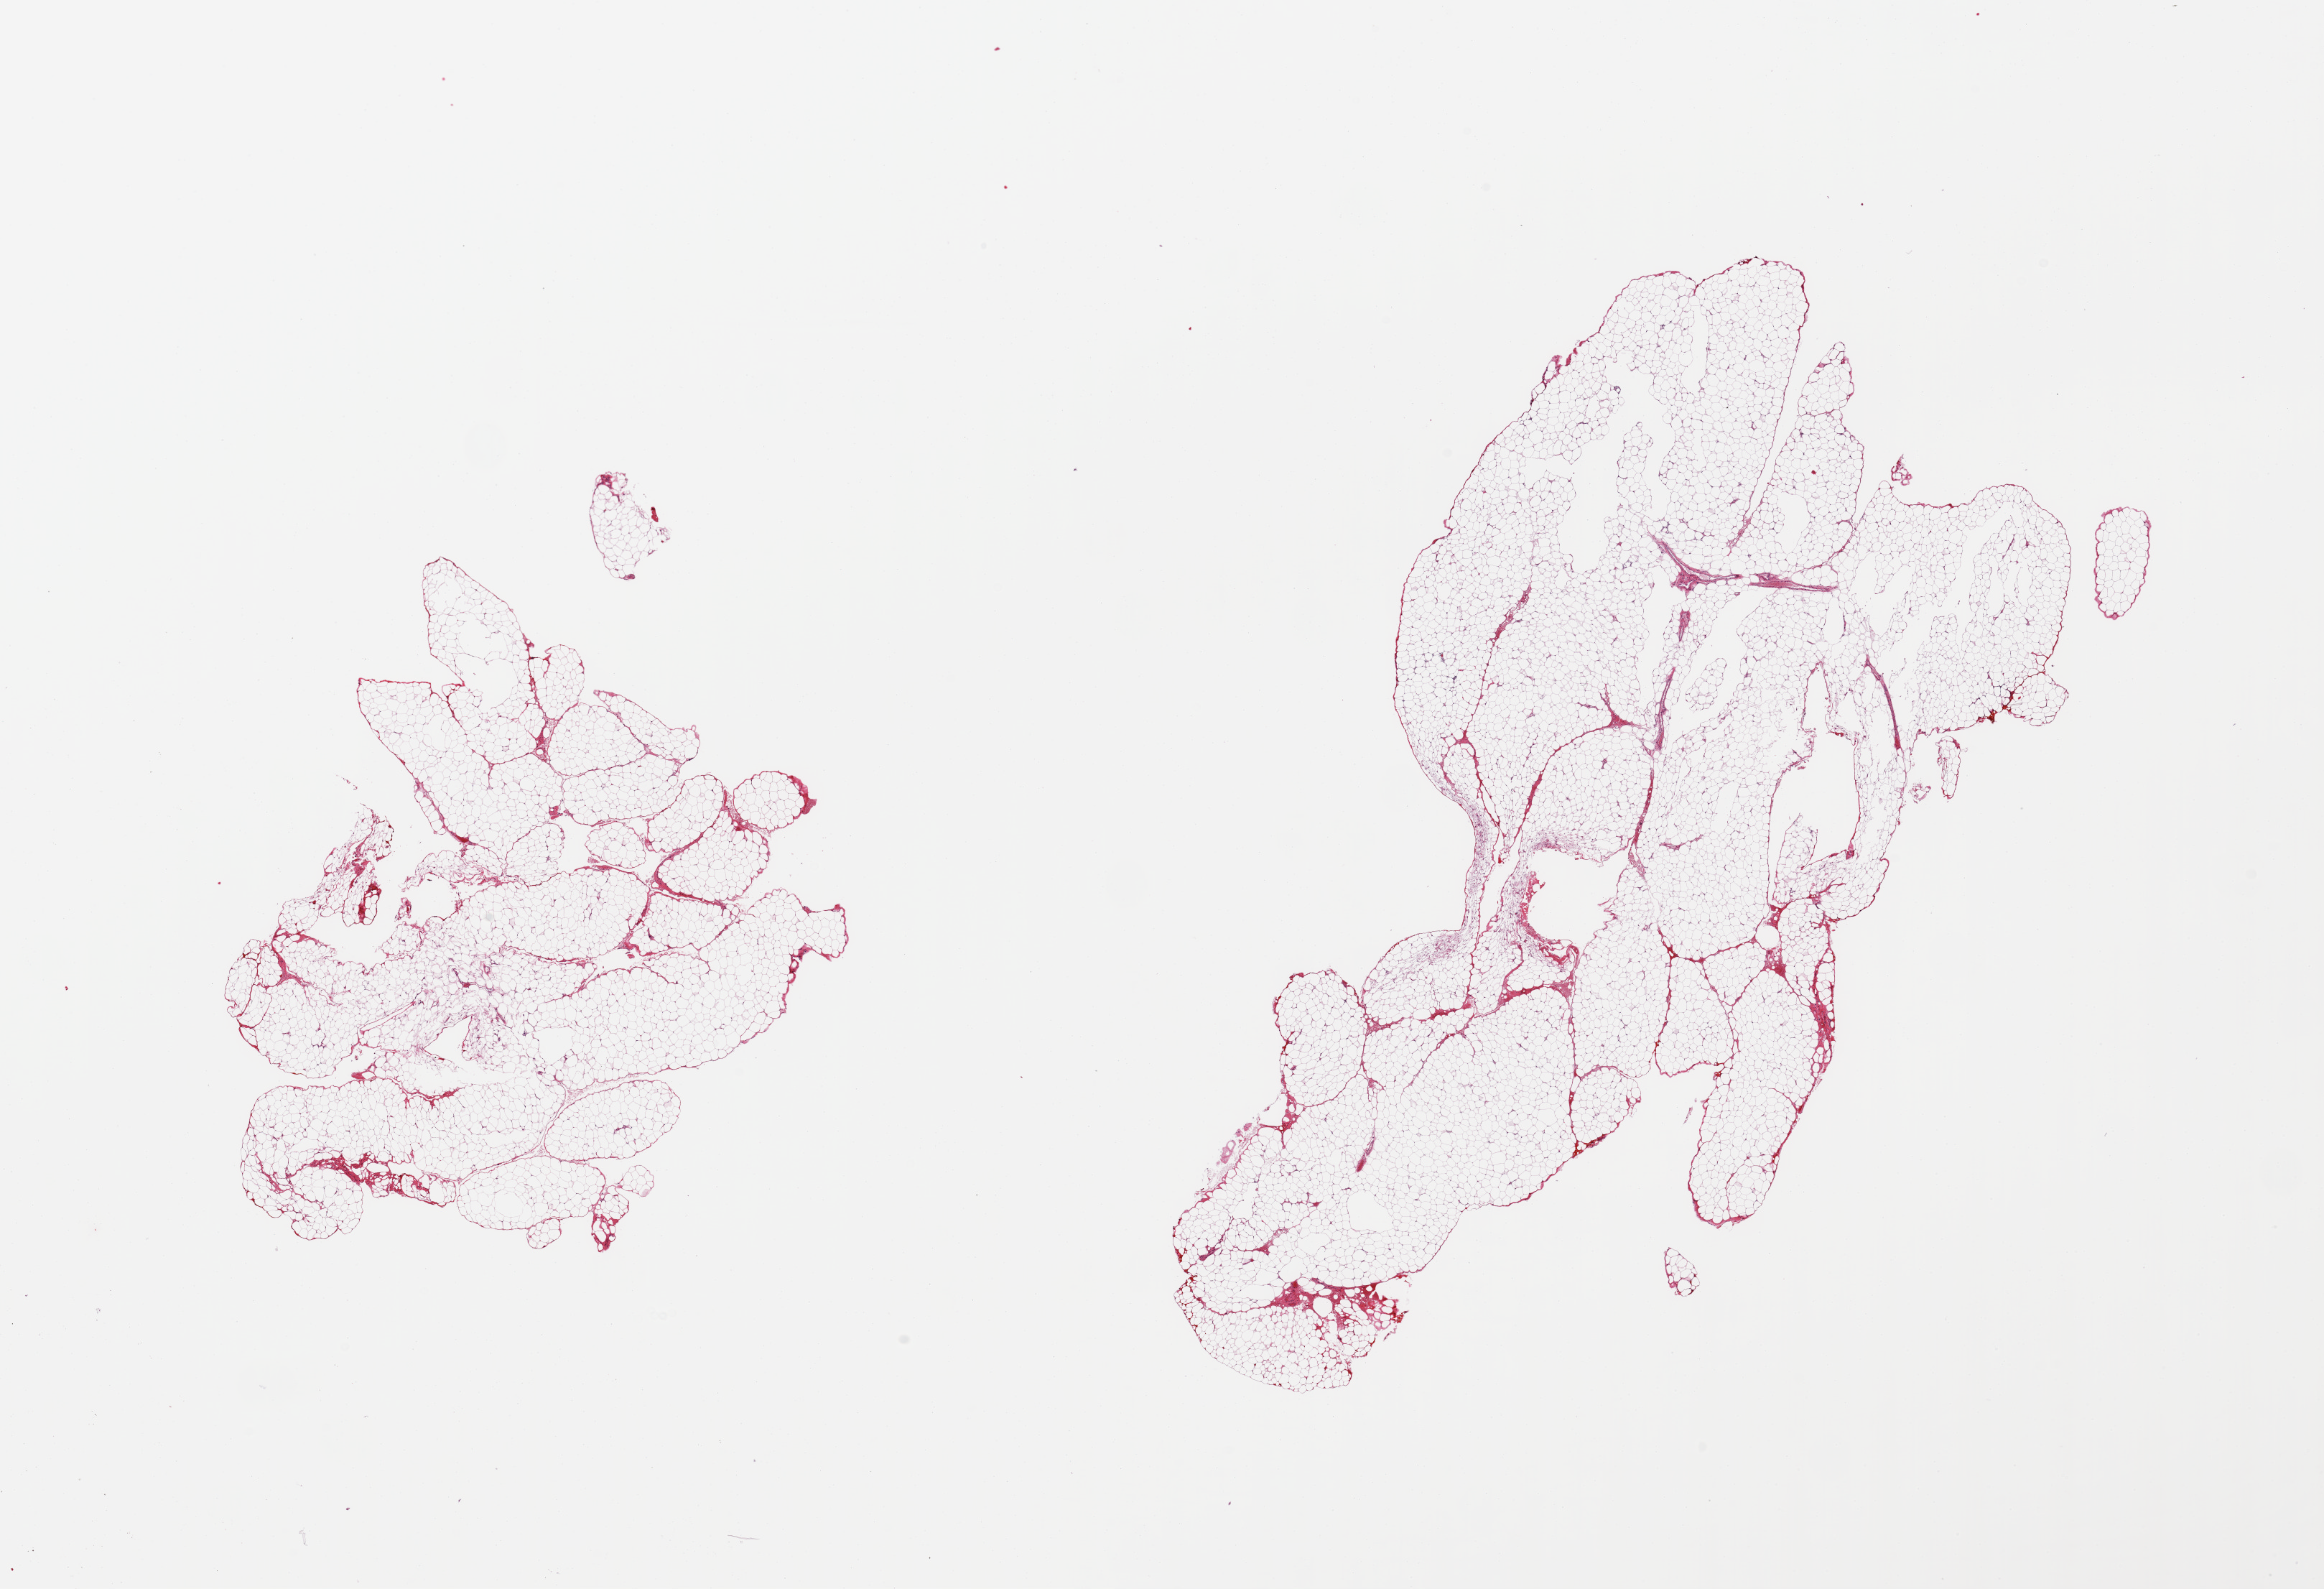
H&E whole-slide image, low-resolution overview of the scanned area, about 25.6 x 17.5 mm (acquisition: 20x scan). PAXgene-fixed, paraffin-embedded tissue. Section of omentum (target tissue). Donor tissue sample. Donor: male.
Review note (as recorded): 2 pieces, trace vascular elements.